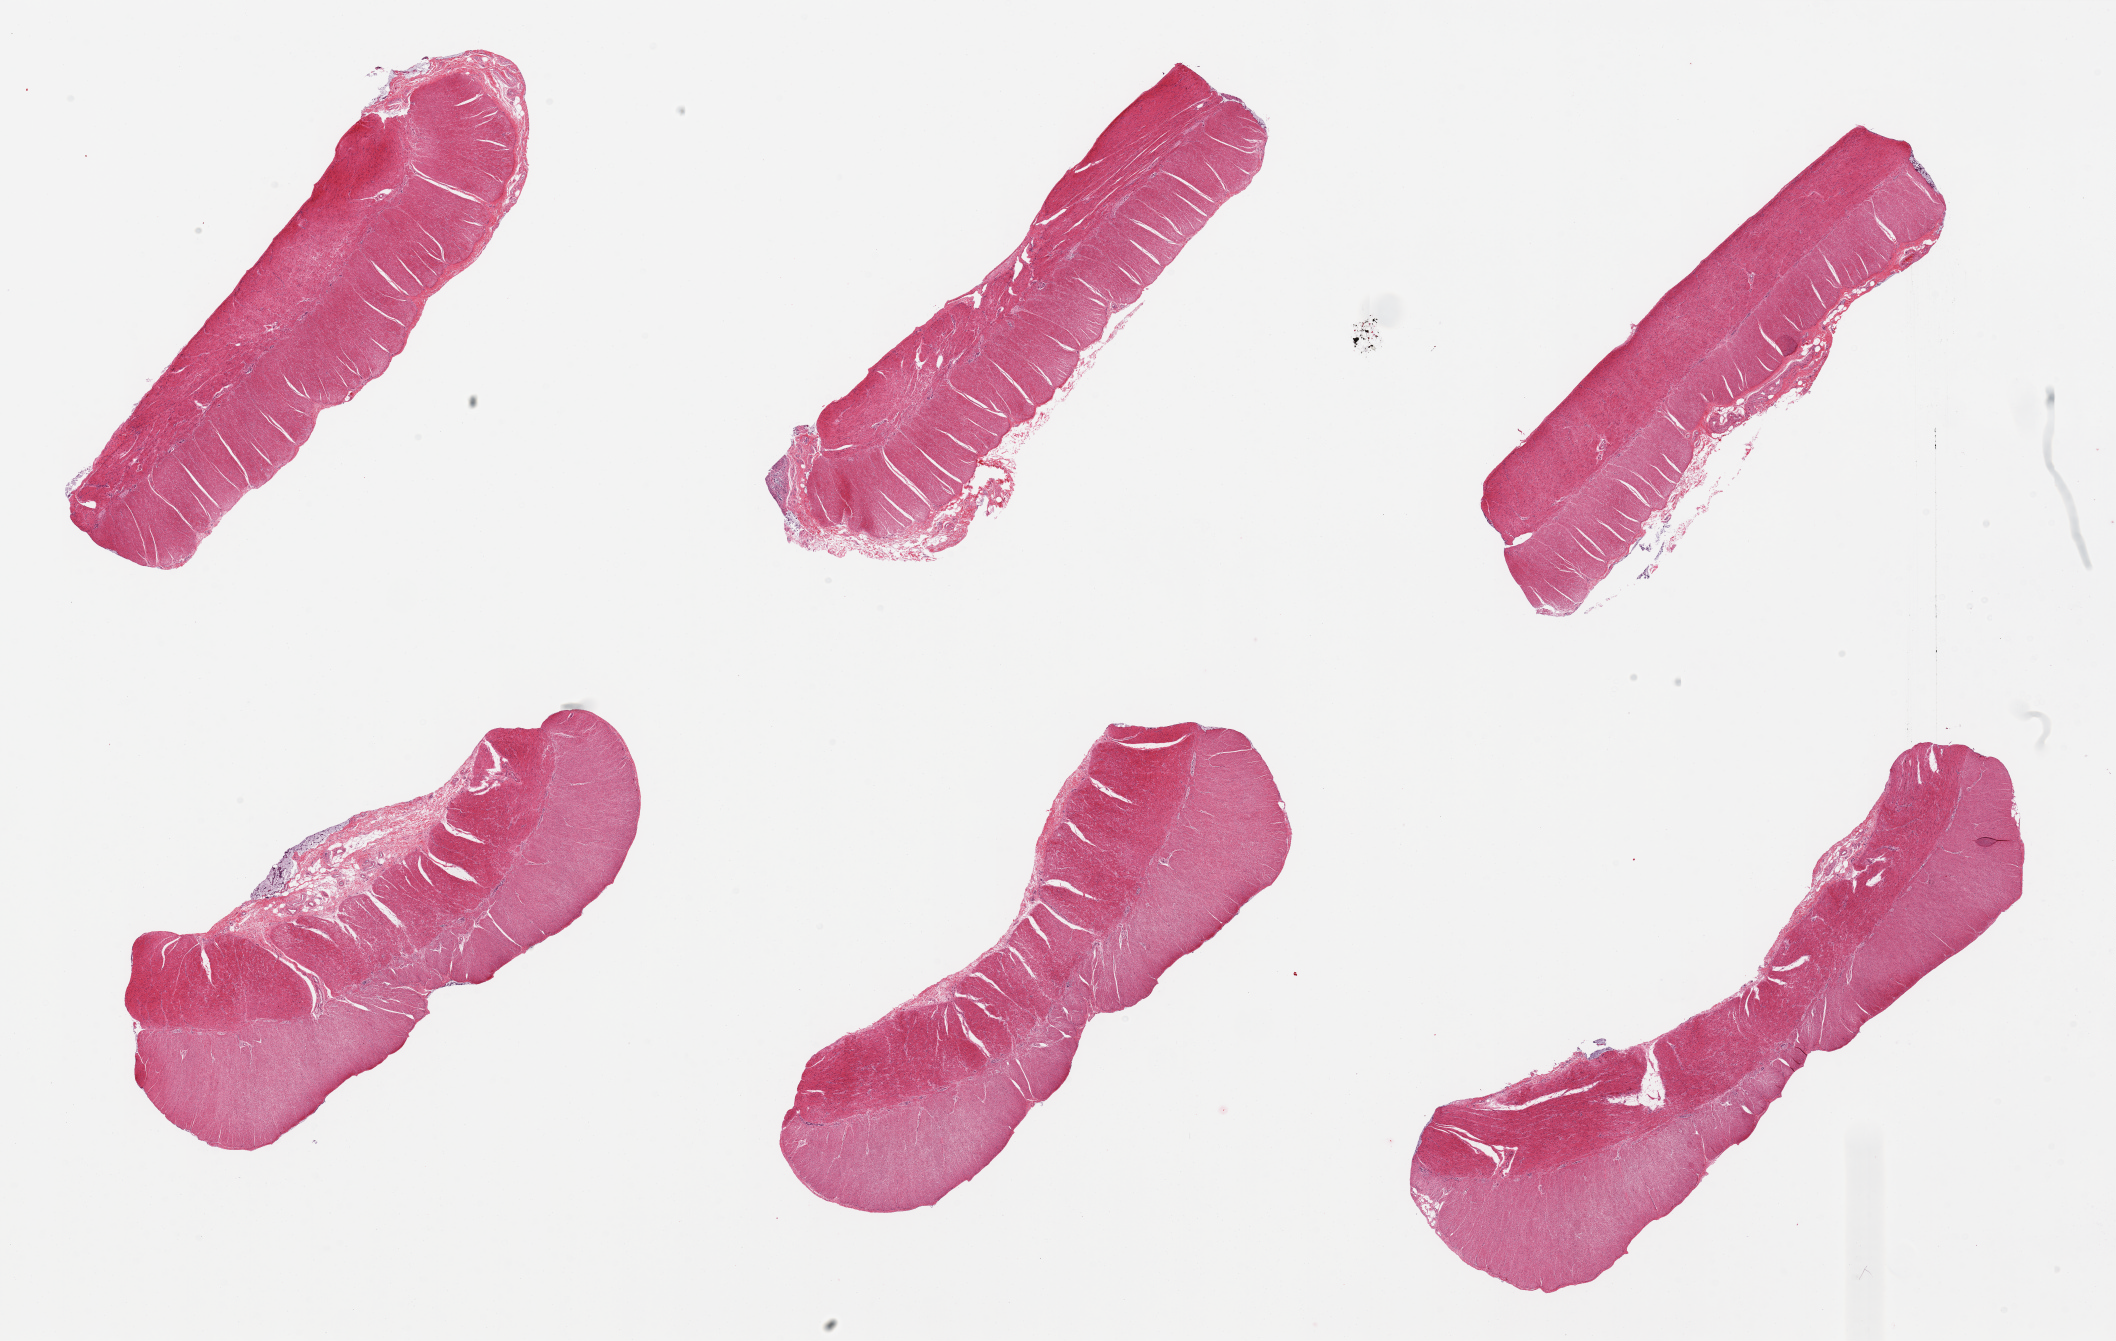
Digitized haematoxylin and eosin-stained section, brightfield — shown as a low-resolution overview of the whole scanned area (about 33.5 x 21.2 mm). PAXgene-fixed paraffin-embedded (PFPE) section. Section of sigmoid colon (target tissue). Tissue donor sample. Donor sex: male.
Reviewer comment on this tissue sample: 6 pieces, congested.